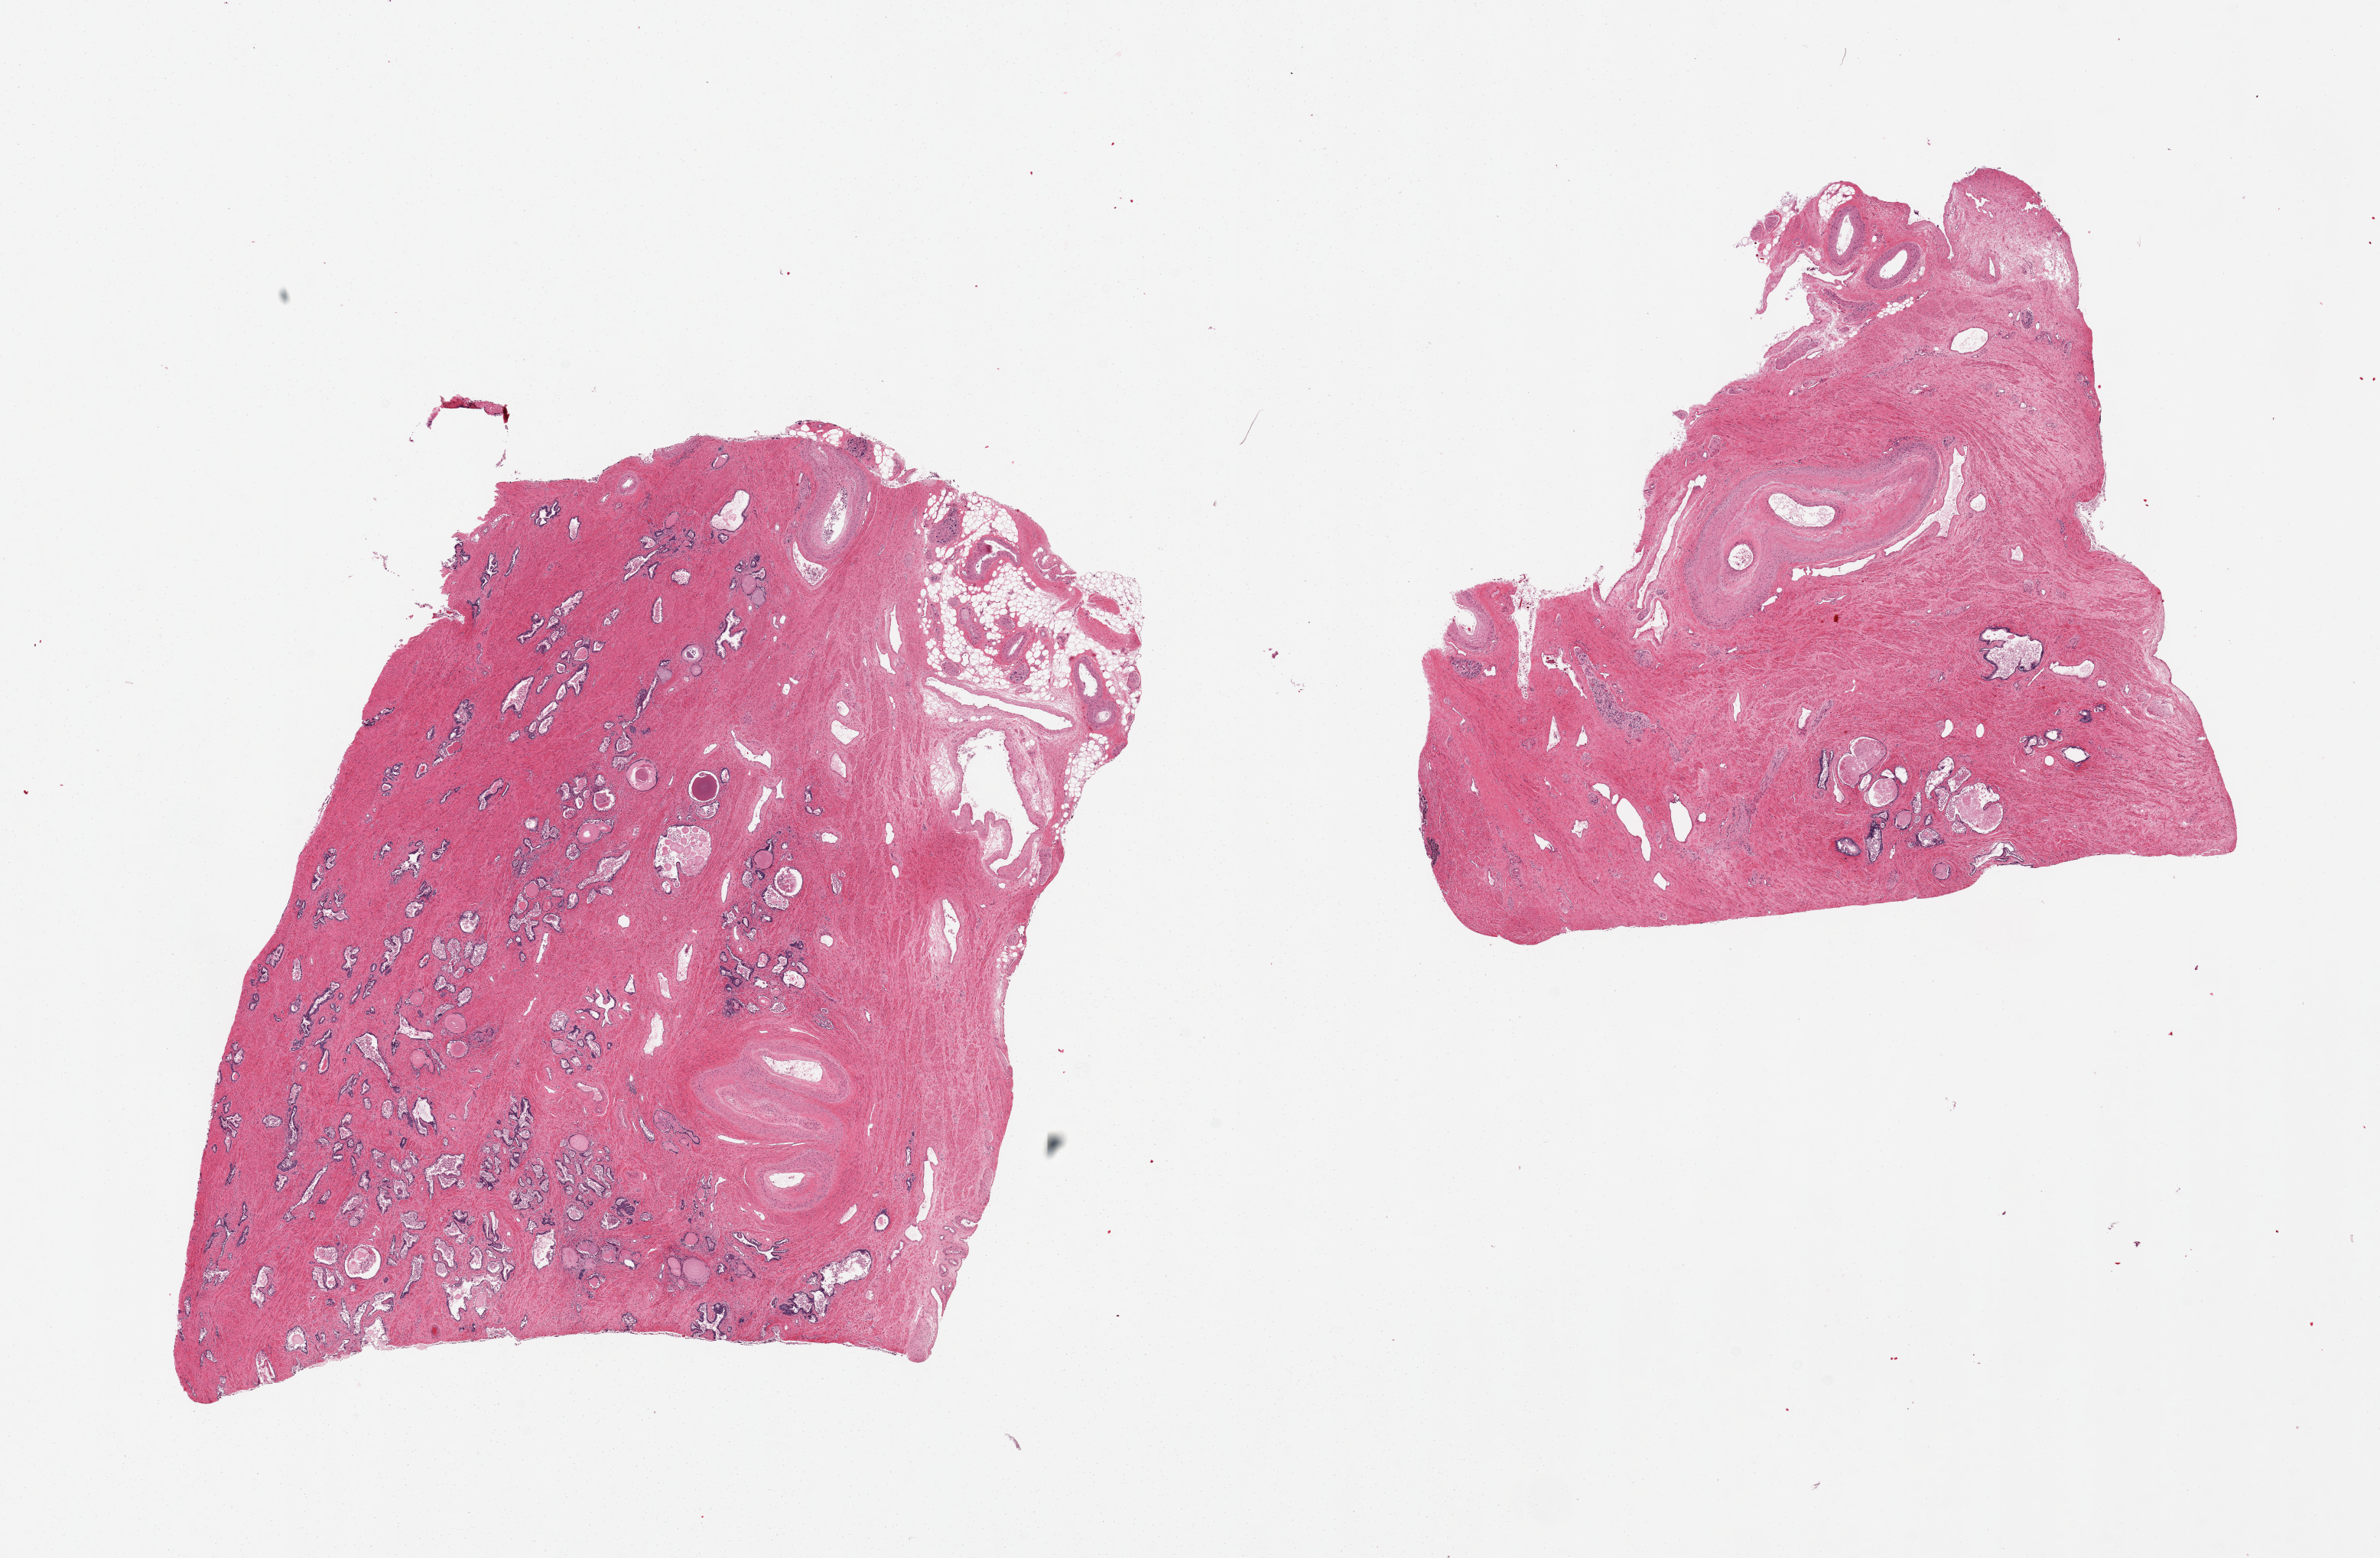
Whole-slide image, hematoxylin and eosin (H&E) stain, low-resolution overview of the scanned area, about 24.6 x 16.1 mm; PAXgene-fixed paraffin-embedded (PFPE) section; section of prostate (target tissue); donor tissue sample. Donor: male.
• reviewer comment on this tissue sample: 2 pieces